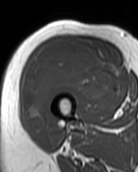
MRI of an extremity soft-tissue mass, one axial slice. Slice 39 of 99 in the series (ordered by position). MR volume resampled by the dataset authors to the PET/CT grid (not the native acquisition matrix). 138 × 172 image matrix, field of view 135 × 168 mm. Female patient. Case-level facts recorded for this patient, not image findings: histological type: pleiomorphic undifferentiated sarcoma; grade: high; site of the primary tumour: right quadricep.
Annotated regions visible in this slice (expert contour drawn on MRI and transferred to this co-registered scan by the dataset authors):
- gross tumour volume including surrounding oedema: box from (x=23, y=41) to (x=113, y=131) px
- gross tumour volume (mass): (x=23, y=41)–(x=113, y=131)